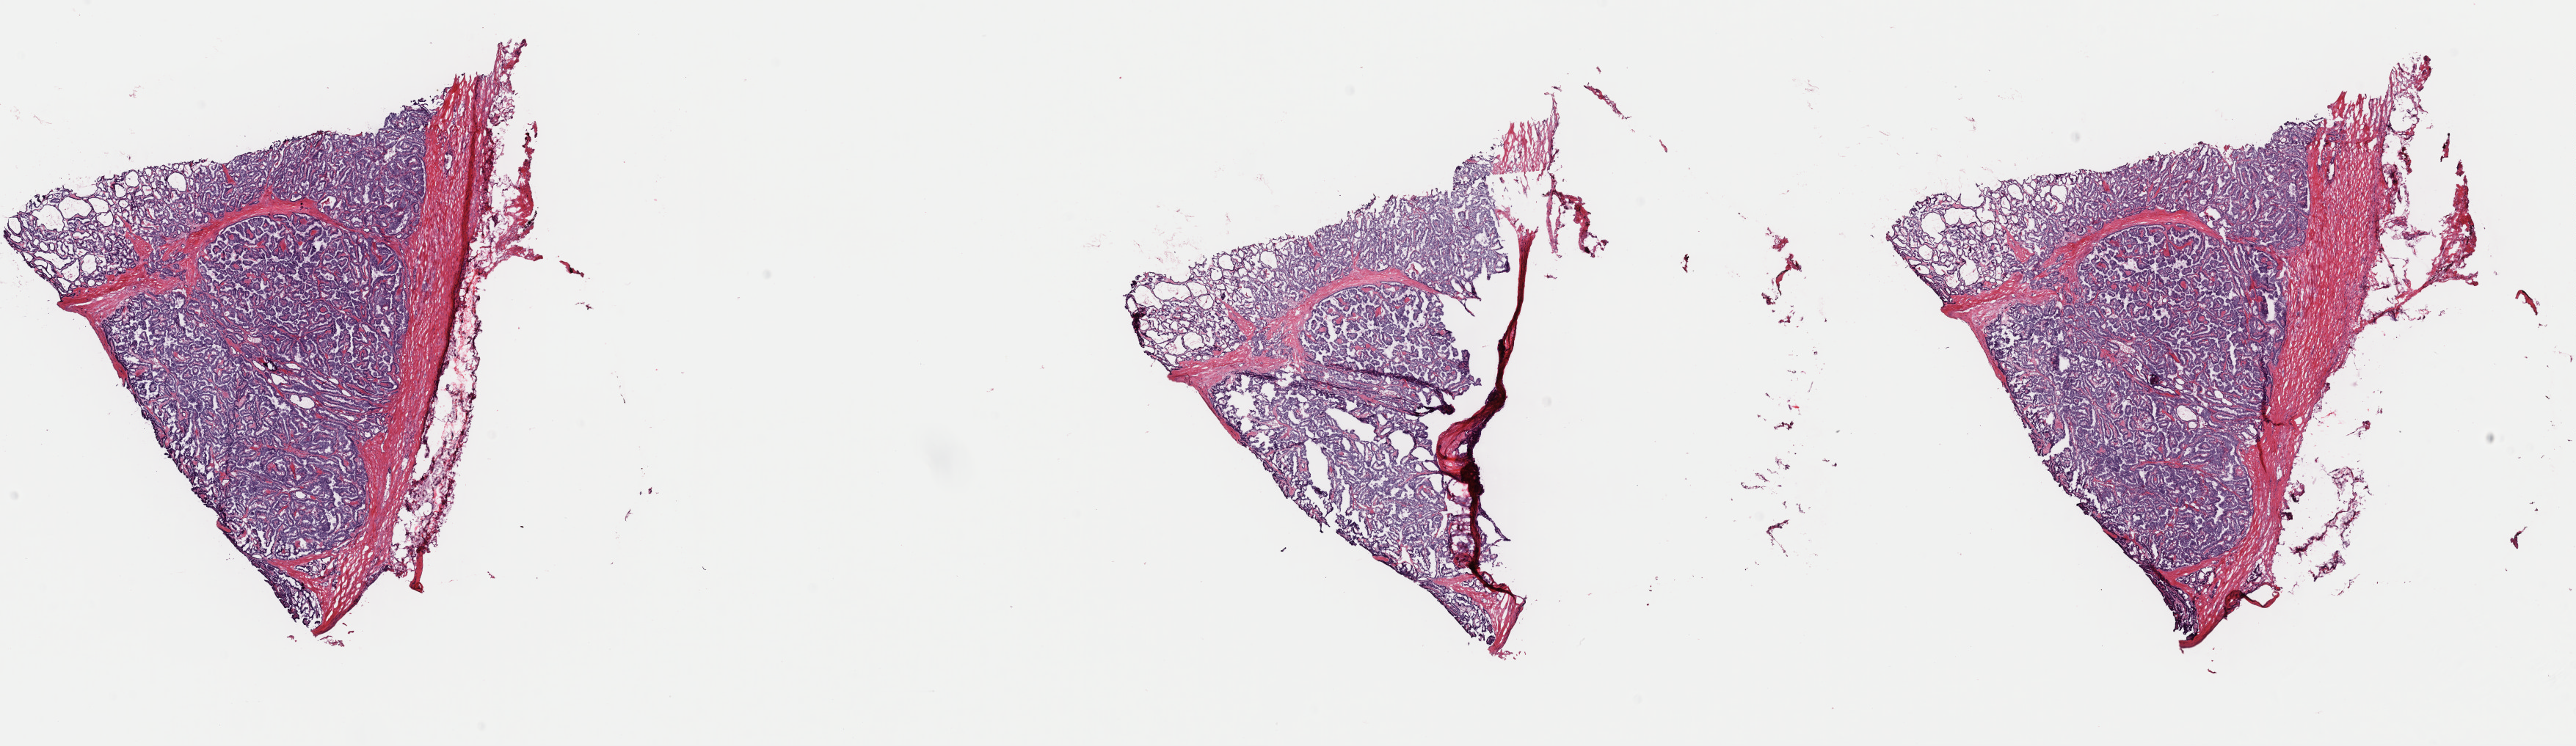
Digitized H&E-stained tissue section (whole slide) — a low-resolution overview of the entire scanned area, about 27.7 x 8.0 mm (acquisition: 40x scan), frozen section from the top of the tissue portion, metastatic tumour sample, sampled site not recorded. Male patient; age at initial diagnosis 39 years. Composition of this section per pathologist review: tumour cells 80%, tumour nuclei 100%, normal cells 0%, stromal cells 20%, necrosis 0%. Infiltration values recorded for this section: lymphocyte infiltration 0%, monocyte infiltration 1%, neutrophil infiltration 0%.
• this section: metastatic tumour tissue
• patient diagnosis: Papillary adenocarcinoma, NOS (primary site: thyroid gland)